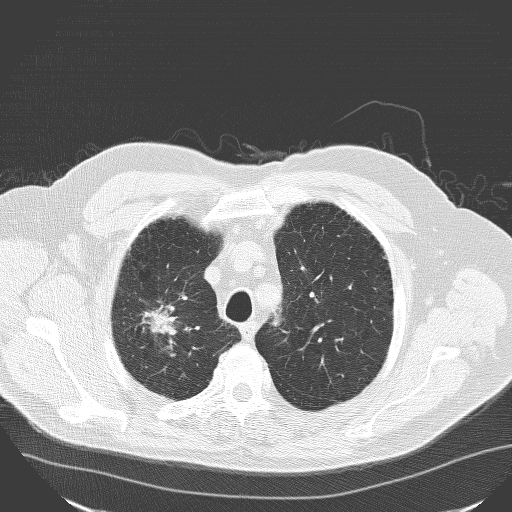
Axial slice from a low-dose chest CT screening exam; baseline annual screen; lung window (W 1500 / L -600 HU); 3.2 mm slice thickness; slice 132 of 160 in the series. Male participant, aged 71 years at enrolment.
Expert-annotated lung lesion, bounding box (x1, y1, x2, y2) in pixels: (115, 278, 189, 355). Screening reader's record for this exam (one nodule recorded; not confirmed to be the boxed lesion): non-calcified nodule or mass ≥4 mm, right upper lobe, 30 × 25 mm, spiculated (stellate) margins, soft tissue attenuation. Lung cancer was diagnosed 182 days after this screen: squamous cell carcinoma, NOS, right upper lobe, poorly differentiated (G3), stage IA (AJCC 6th edition), 30 mm at pathology.